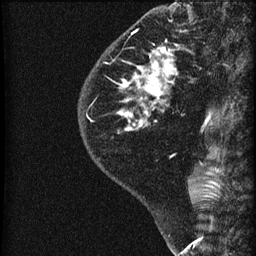
Breast MRI (dynamic contrast-enhanced), one sagittal slice. Slice 19 of 60 in the series (ordered by position). Dynamic contrast-enhanced series, image 2 of 3 at this slice position (ordered by acquisition). 1.5 T. TE 4.2 ms, TR 22.7 ms. 1.8 mm slice thickness. 256 × 256 image matrix, field of view 180 × 180 mm. Patient: female, 45 years. Case-level facts recorded for this patient, not image findings: setting: breast cancer imaged before/during neoadjuvant chemotherapy; receptor status: HR-positive, HER2-negative.
Annotated regions visible in this slice (semi-automatic segmentation, software-assisted and operator-edited):
- analysis volume of interest (the breast-tissue region the enhancement analysis was run in; not a lesion): bounding box [x1, y1, x2, y2] px = [78, 11, 205, 140]
- tumour enhancement mask (voxels above the 90 % enhancement threshold inside the analysis volume of interest): [120, 47, 177, 130]